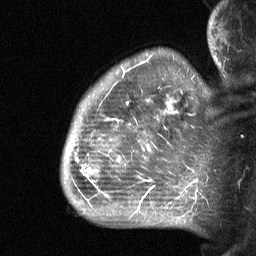
Breast MRI (dynamic contrast-enhanced), one sagittal slice; position 50 of 64 along the scan axis; dynamic contrast-enhanced study with each time point stored as its own series, time point 2 of 3 at this slice position (early post-contrast, ordered by acquisition time); 1.5 T; TE 4.8 ms, TR 27 ms; 2.3 mm slice thickness; 256 × 256 image matrix. Female patient, age 50 years. From the clinical record (not read from this slice): setting: breast cancer imaged before/during neoadjuvant chemotherapy; receptor status: HER2-positive.
Annotated regions visible in this slice (semi-automatic segmentation, software-assisted and operator-edited):
- analysis volume of interest (the breast-tissue region the enhancement analysis was run in; not a lesion): bounding box [x1, y1, x2, y2] px = [60, 64, 211, 218]
- tumour enhancement mask (voxels above the 90 % enhancement threshold inside the analysis volume of interest): [76, 99, 178, 196]